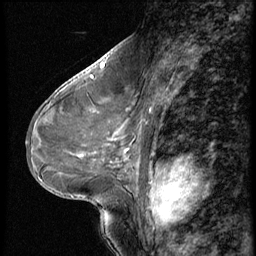
Breast MRI (dynamic contrast-enhanced), one sagittal slice. Position 30 of 56 along the scan axis. Dynamic contrast-enhanced series, image 2 of 3 at this slice position (ordered by acquisition). 1.5 T. TE 4.2 ms, TR 9 ms. 2.5 mm slice thickness. 256 × 256 image matrix. Patient: female, 46 years. Case-level facts recorded for this patient, not image findings: setting: breast cancer imaged before/during neoadjuvant chemotherapy; receptor status: HER2-positive.
Outlined on this slice (semi-automatic segmentation, software-assisted and operator-edited):
- analysis volume of interest (the breast-tissue region the enhancement analysis was run in; not a lesion): bounding box [x1, y1, x2, y2] px = [64, 98, 174, 182]
- tumour enhancement mask (voxels above the 140 % enhancement threshold inside the analysis volume of interest): [157, 167, 174, 182]